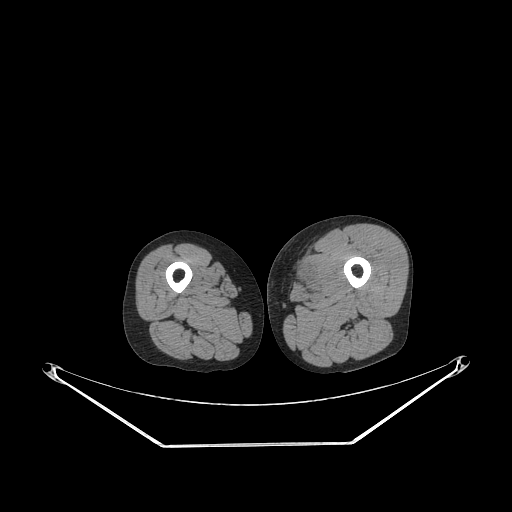
CT of an extremity soft-tissue mass (from a PET/CT study), one axial slice; position 231 of 267 along the scan axis; reconstruction kernel STANDARD; soft-tissue window (W 400 / L 40 HU); 3.75 mm slice thickness; 512 × 512 image matrix. Male patient. Case-level facts recorded for this patient, not image findings: histological type: pleiomorphic leiomyosarcoma; grade: high; site of the primary tumour: left thigh.
Structures marked on this image (expert contour drawn on MRI and transferred to this co-registered scan by the dataset authors):
- gross tumour volume including surrounding oedema: bounding box [x1, y1, x2, y2] px = [290, 258, 314, 291]
- gross tumour volume (mass): [297, 276, 307, 287]